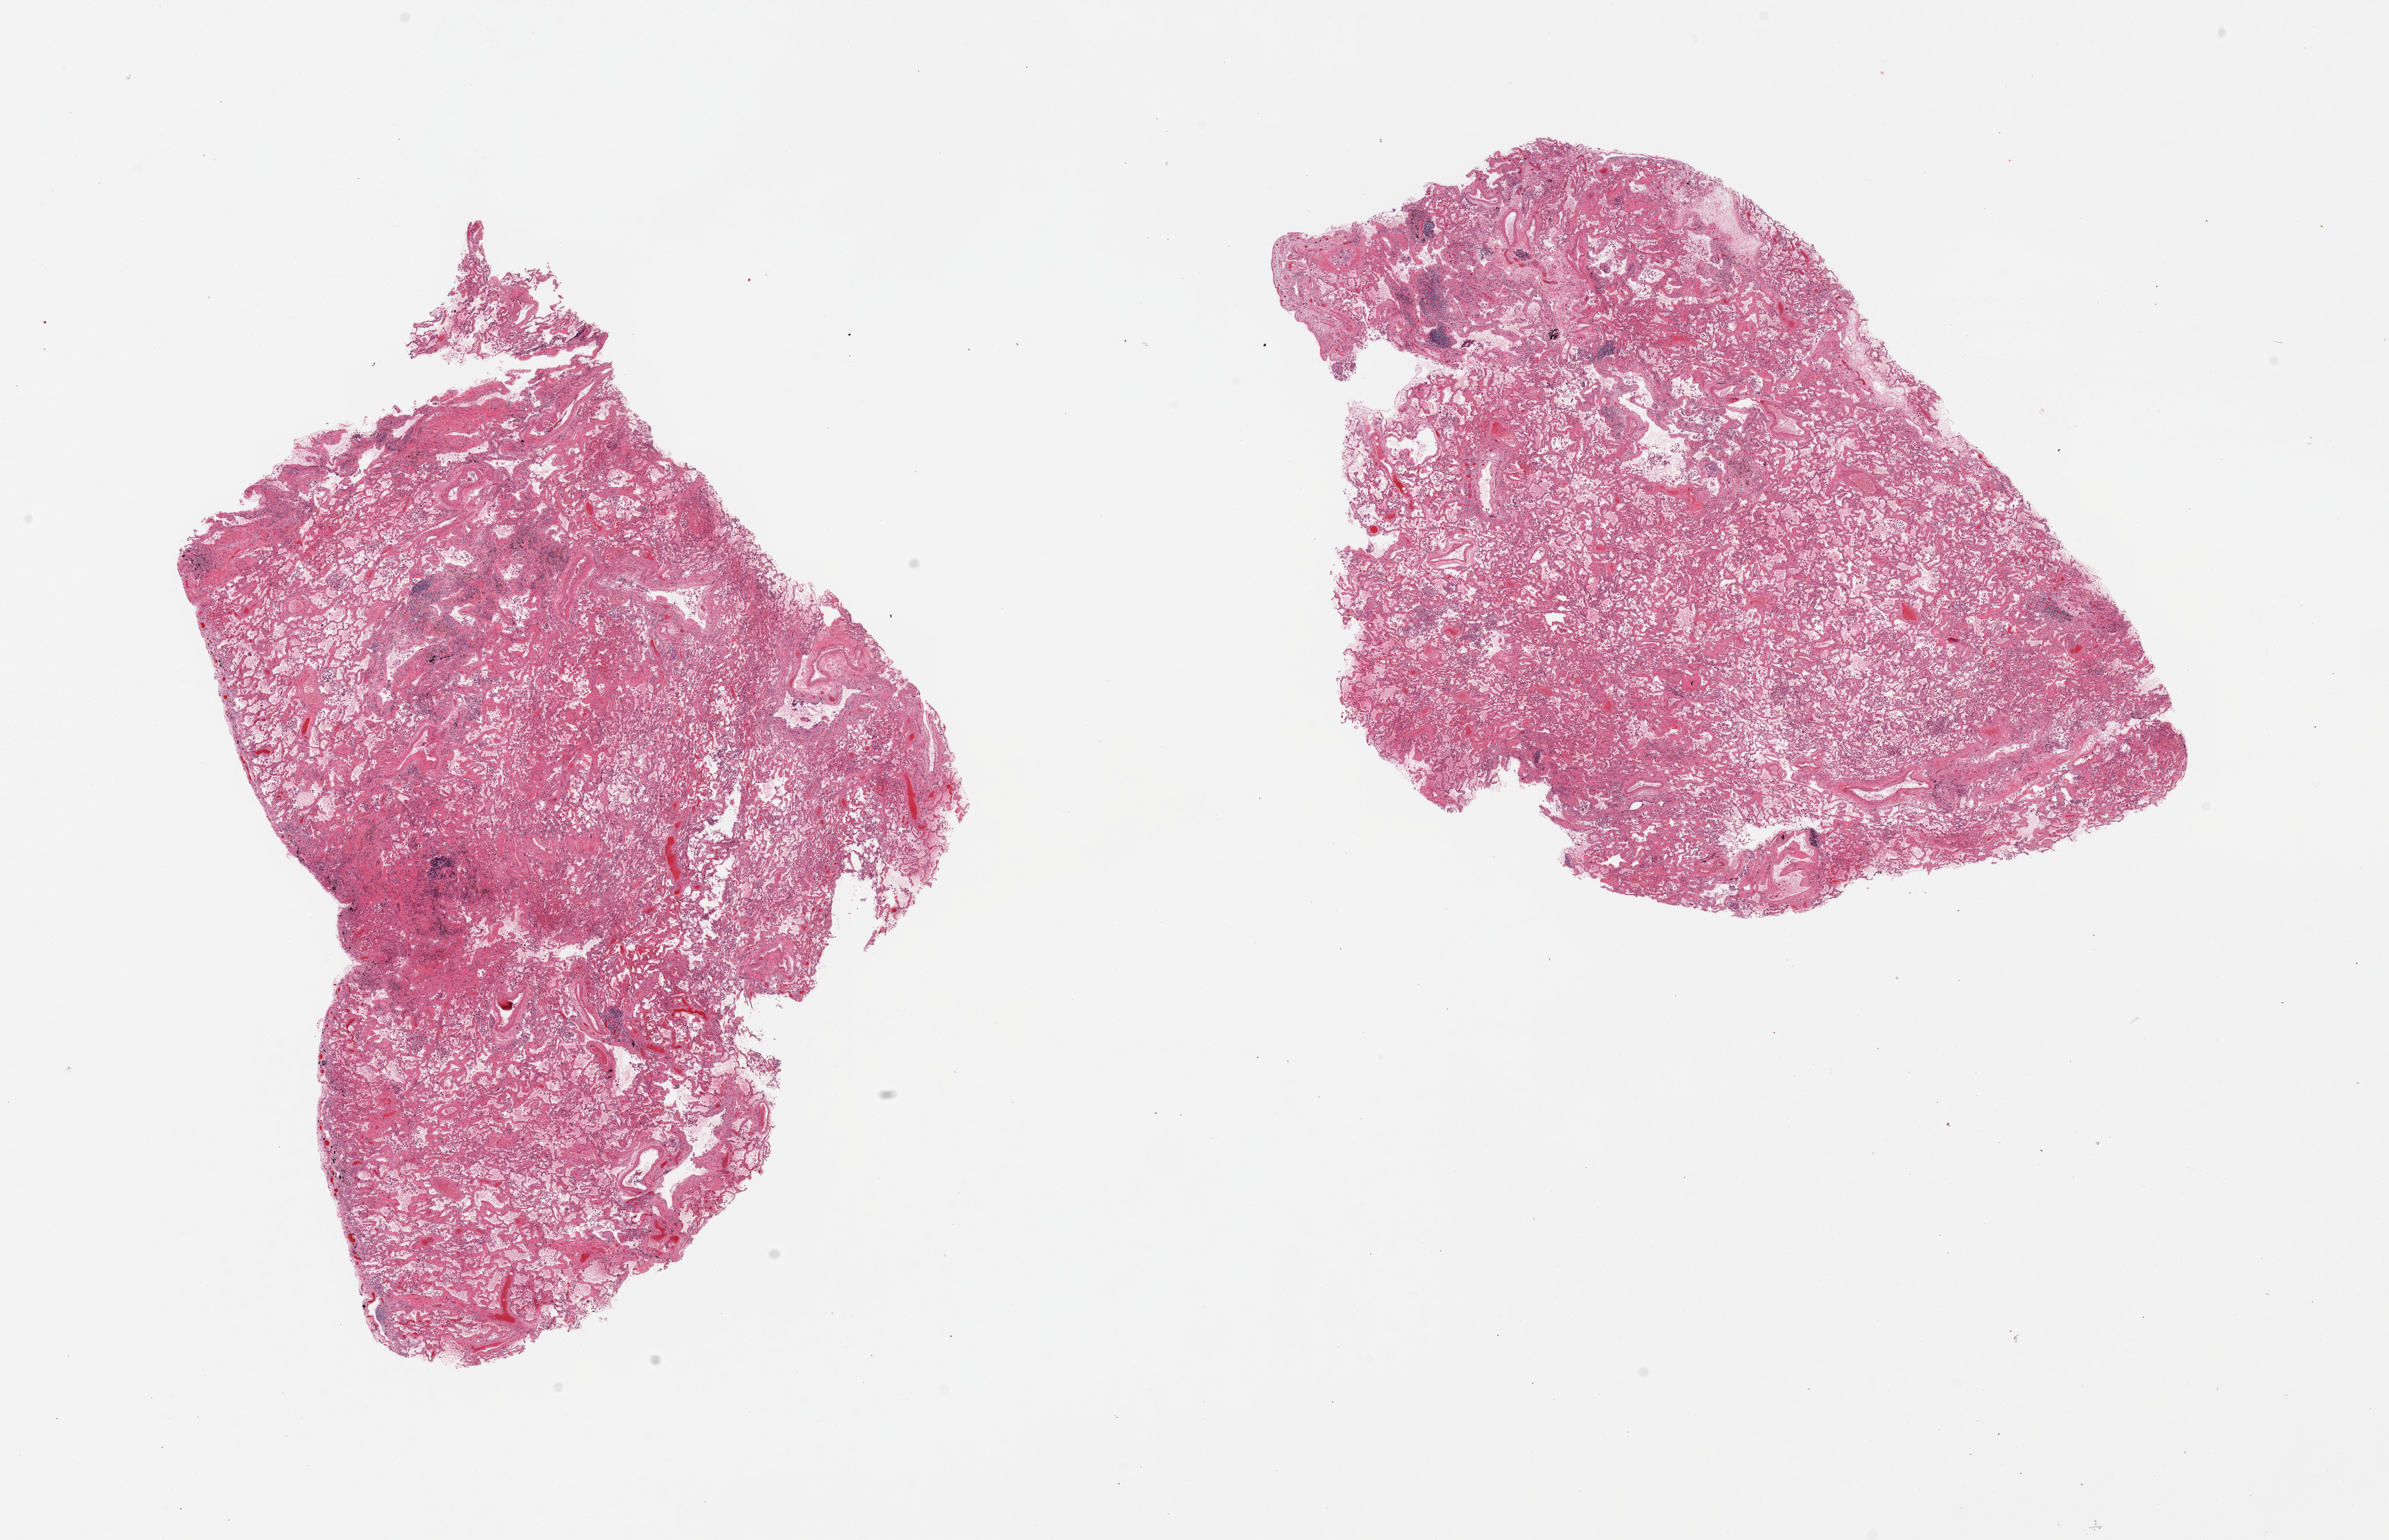
H&E whole-slide image, low-resolution overview of the scanned area, about 27.6 x 17.8 mm (from a 20x scan), PAXgene-fixed paraffin-embedded (PFPE) section, target tissue: lung, tissue donor sample.
Pathologist's review note for this sample: 2 pieces; patchy fibrosis; pulmonary edema; numerous alveolar macrophages.